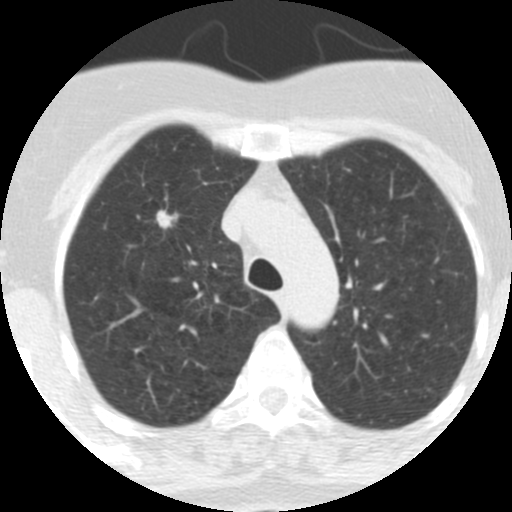
Low-dose screening chest CT, one axial slice. Slice 240 of 313 in the series (ordered by position). Reconstruction kernel STANDARD. 120 kVp. Lung window (W 1500 / L -600 HU). 512 × 512 image matrix, field of view 253 × 253 mm.
Structures marked on this image (manually delineated by an expert):
- lesion 1 (tumor, upper lobe of right lung): bounding box <156,210,178,229> (left, top, right, bottom; pixels)